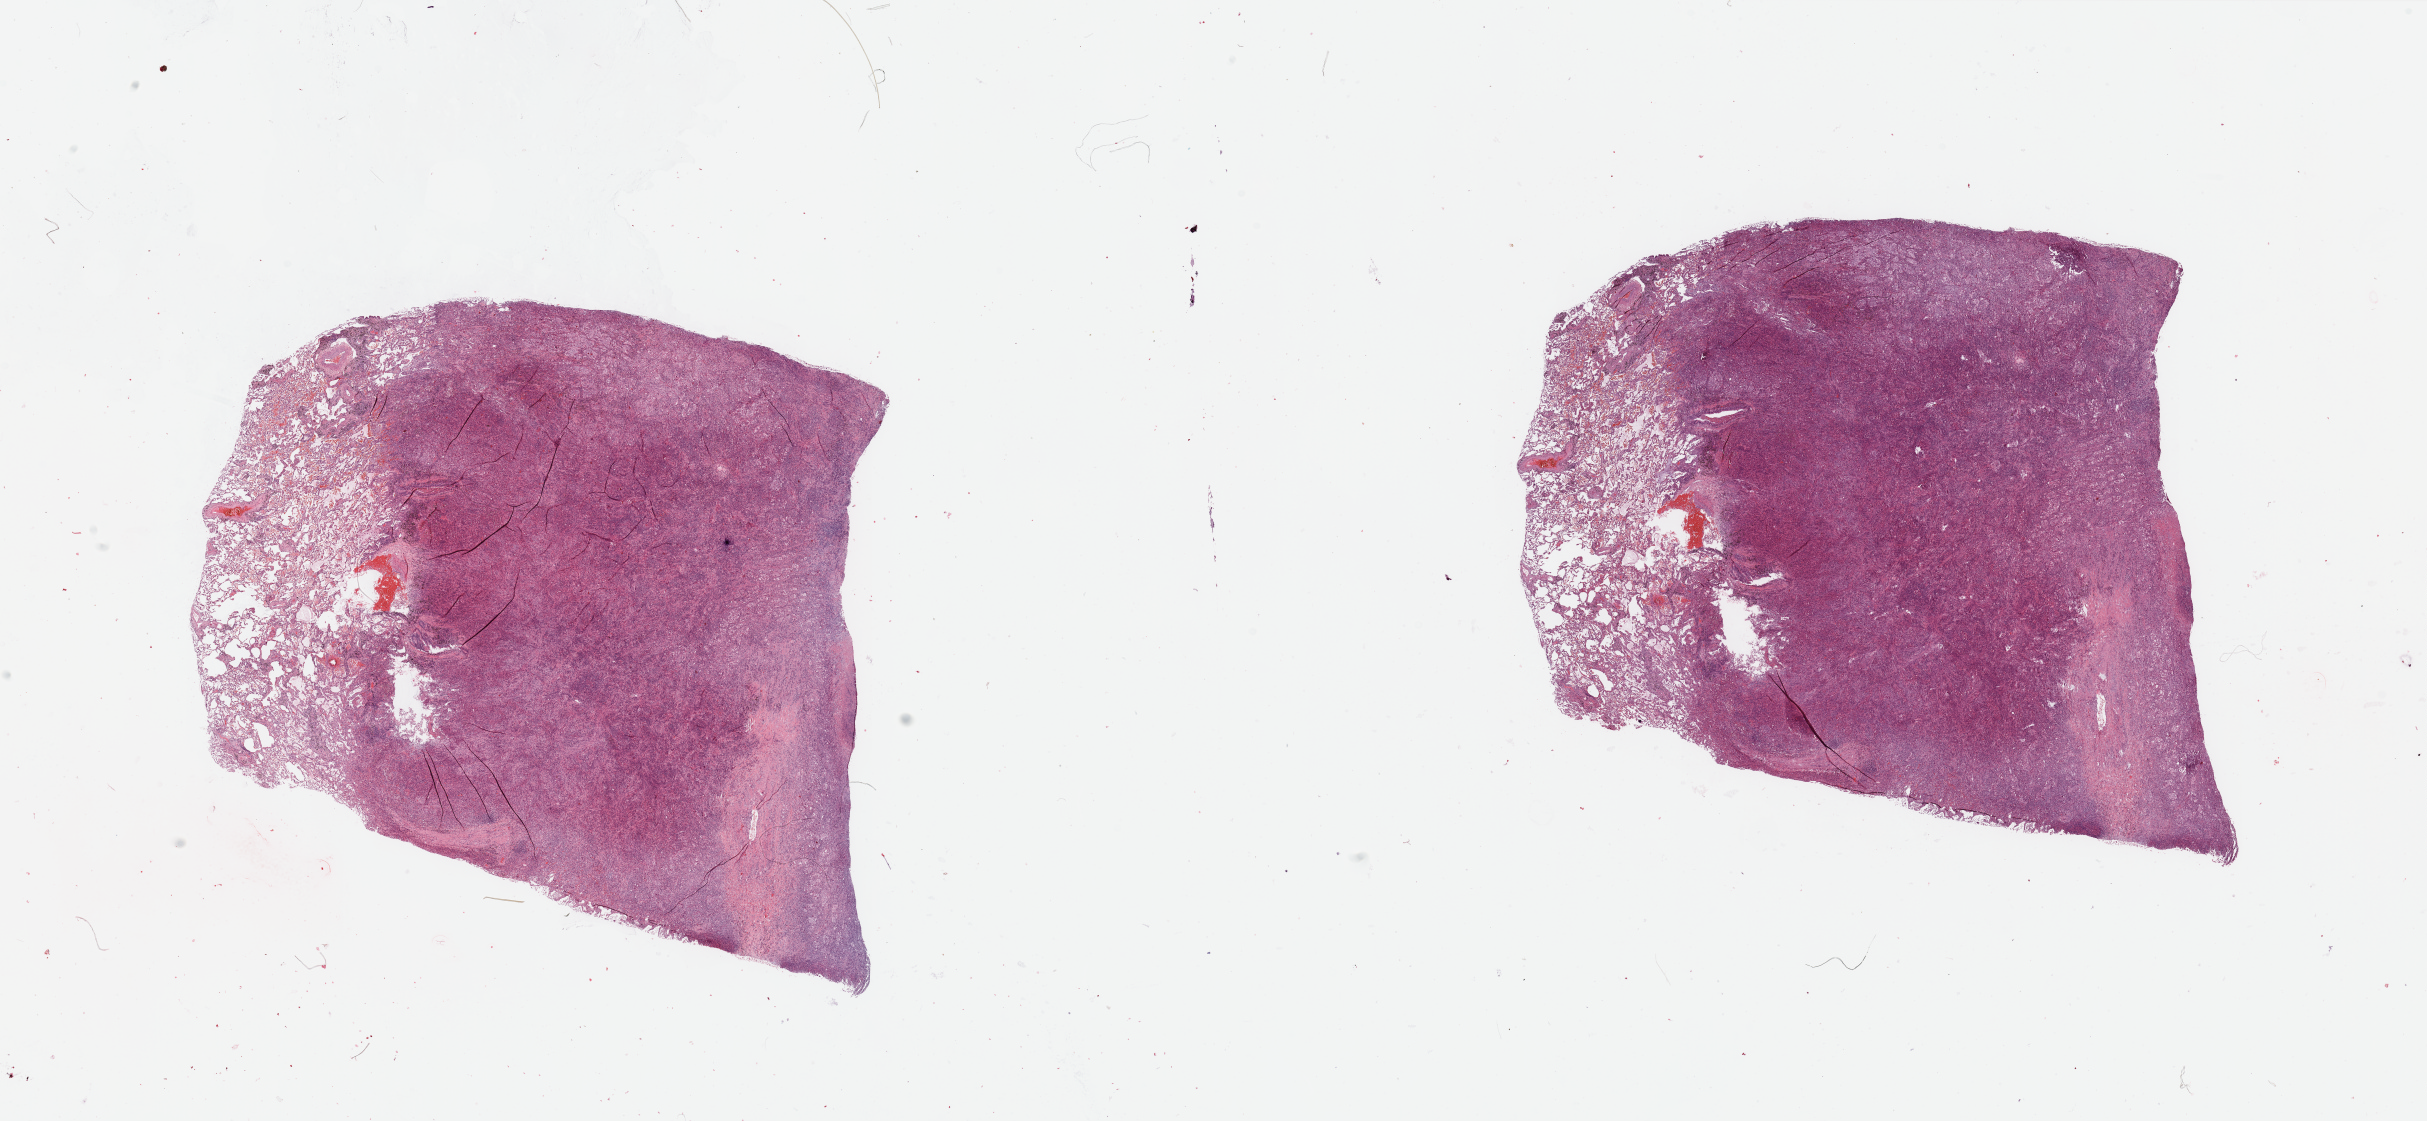
Digitized Hematoxylin and eosin (H&E) stained tissue section (whole slide), whole scanned area (about 38.4 x 17.7 mm, acquisition: 20x scan) shown as a low-resolution overview. Lung, tumour tissue. 65-year-old male patient. Histologic grade: G3 (poorly differentiated).
Diagnosis: Adenocarcinoma, NOS. AJCC pathologic stage: IIIA.